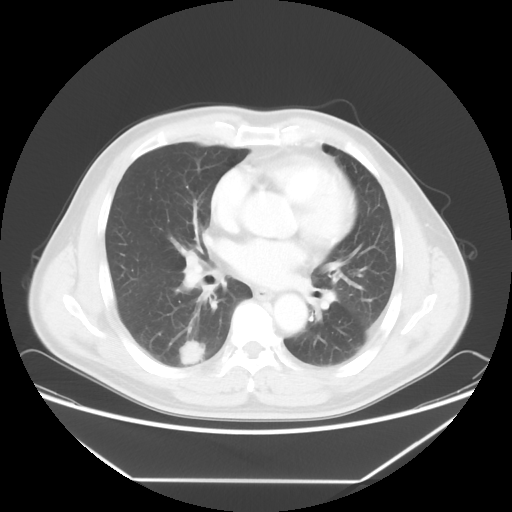
Chest CT, one axial slice. Slice 34 of 65 in the series (ordered by position). Reconstruction kernel STANDARD. Lung window (W 1500 / L -600 HU). 5 mm slice thickness. 512 × 512 image matrix. Male patient, age 50 years. Case-level facts recorded for this patient, not image findings: clinical TNM (as recorded): T1c N0 M0.
Annotated regions visible in this slice (bounding box drawn by a radiologist):
- lung tumour (recorded histology: adenocarcinoma): bounding box [x1, y1, x2, y2] px = [173, 339, 211, 368]